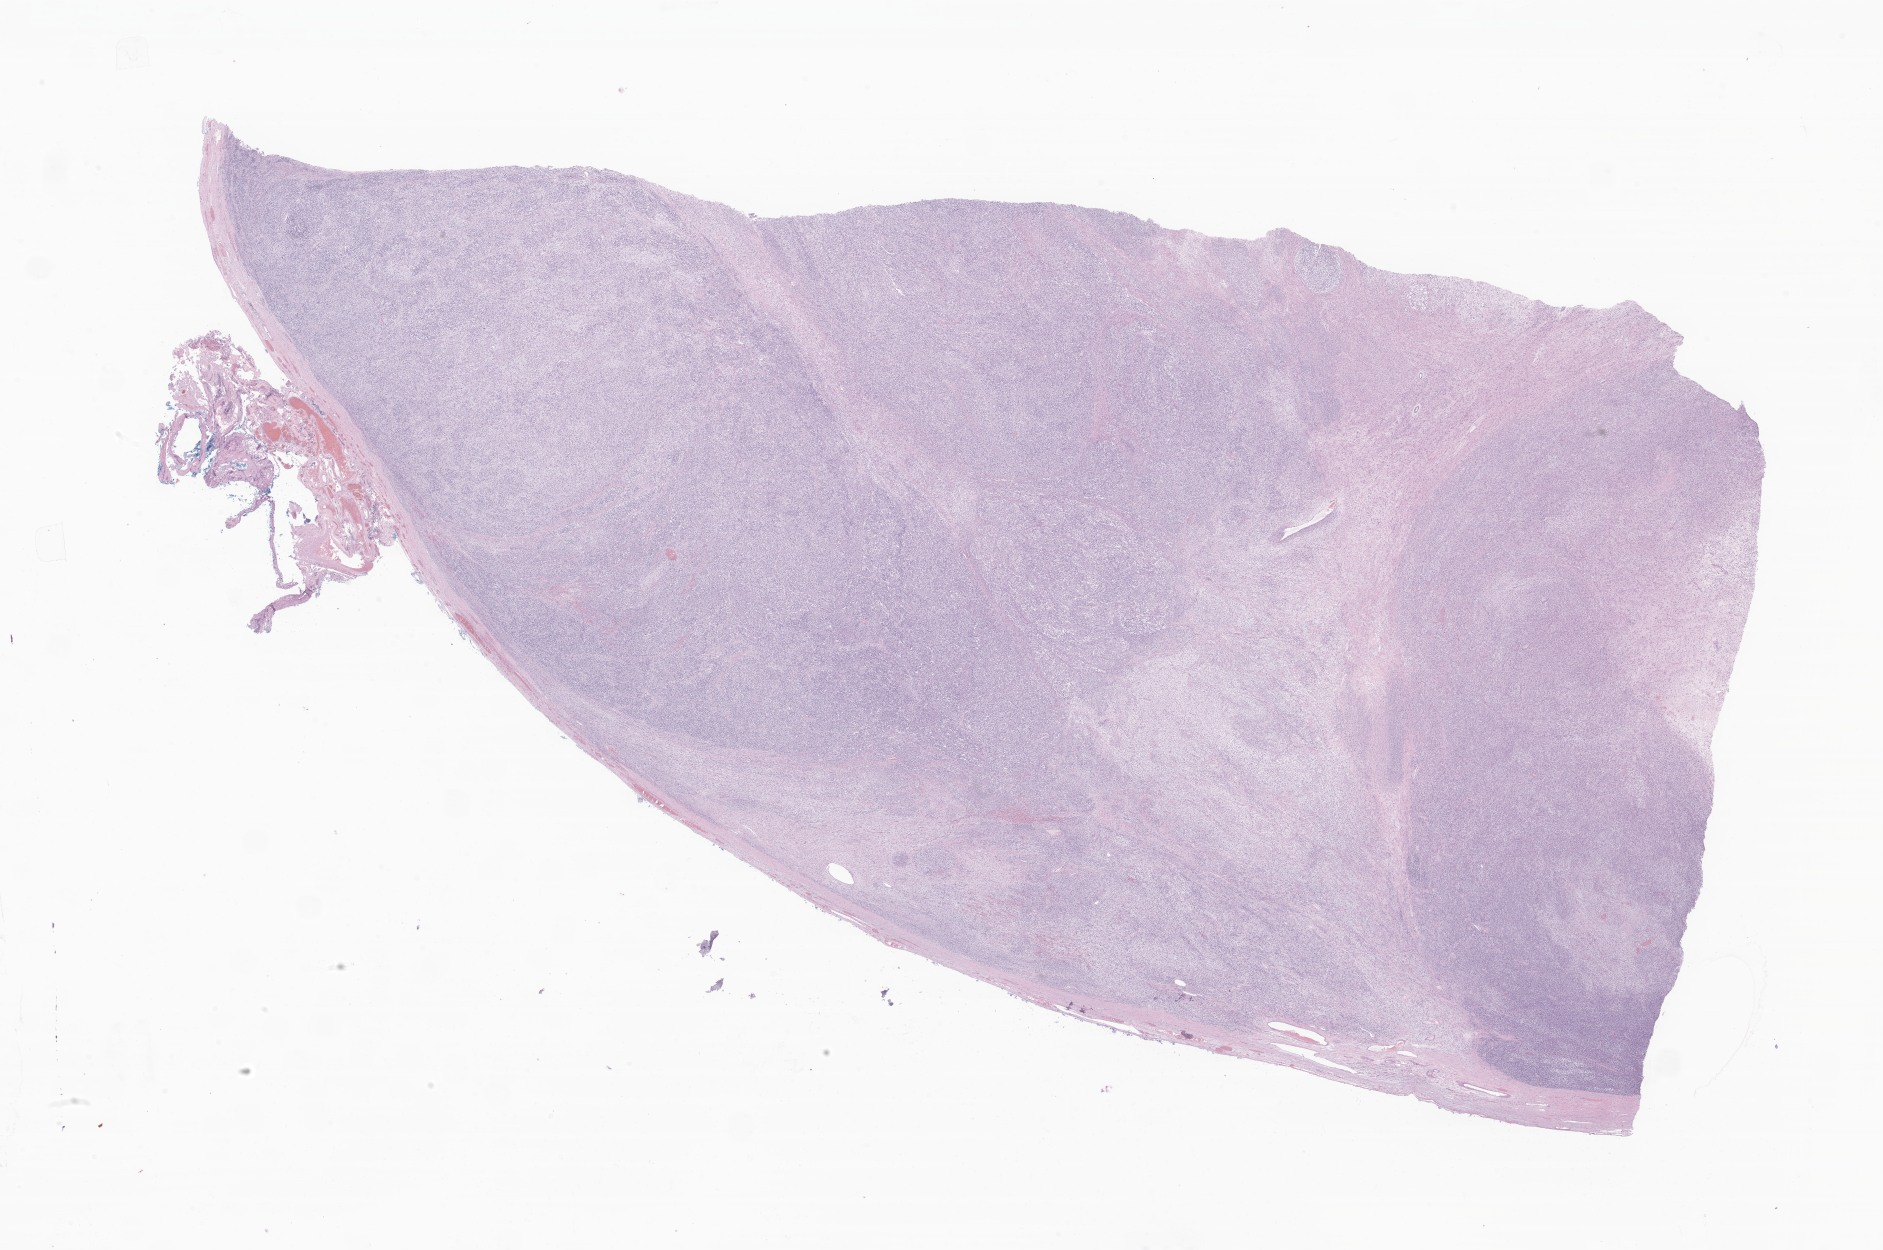
Hematoxylin and eosin (H&E) whole-slide image of tumor tissue from the kidney — low-resolution overview of the scanned area, about 31.8 x 21.1 mm, formalin-fixed, paraffin-embedded (FFPE) tissue. Patient: male, age 56 months (4 years 8 months).
* recorded diagnosis: Malignant peripheral nerve sheath tumor w. rhabdomyoblastic diff